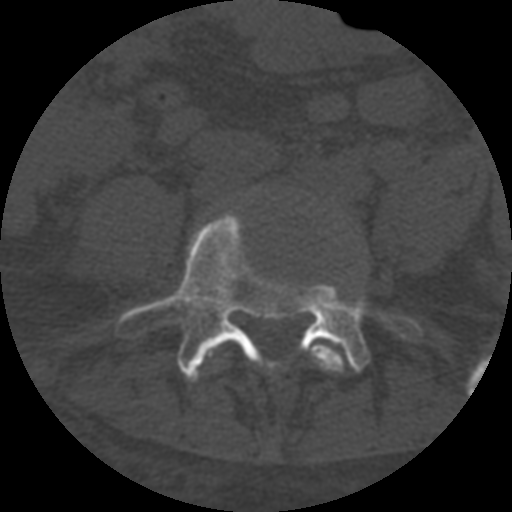
CT including the spine, one axial slice; slice 192 of 708 in the series (ordered by position); reconstruction kernel STANDARD; one of 3 acquisitions stored at this slice position; bone window (W 1800 / L 400 HU); 1.25 mm slice thickness; 512 × 512 image matrix. Patient age 55 years. From the clinical record (not read from this slice): primary cancer: colon.
Outlined on this slice (semi-automatic segmentation, software-assisted and operator-edited):
- L4 vertebra: bounding box [x1, y1, x2, y2] px = [220, 336, 345, 373]
- L5 vertebra: [114, 213, 425, 383]